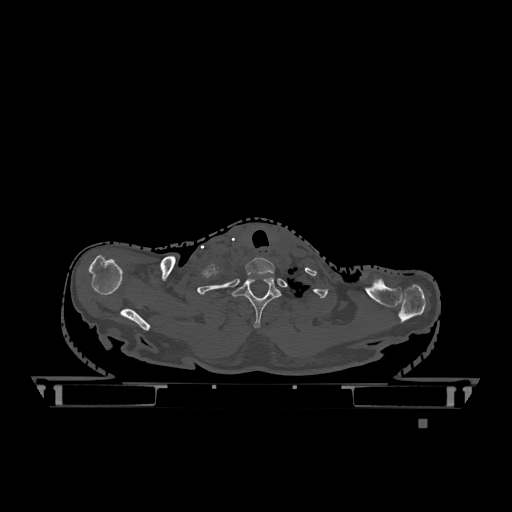
CT including the spine, one axial slice. Slice 1001 of 1317 in the series (ordered by position). Bone window (W 1800 / L 400 HU). 0.5 mm slice thickness. 512 × 512 image matrix, field of view 500 × 500 mm. Female patient, age 74 years. Case-level facts recorded for this patient, not image findings: primary cancer: lung.
Outlined on this slice (semi-automatically segmented with operator editing):
- T1 vertebra: bounding box <232,276,281,328> (left, top, right, bottom; pixels)